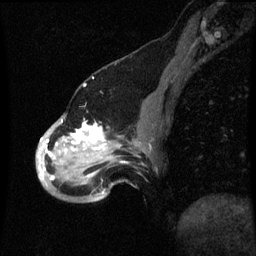
Breast MRI (dynamic contrast-enhanced), one sagittal slice; position 20 of 60 along the scan axis; dynamic contrast-enhanced series, image 2 of 3 at this slice position (ordered by acquisition); 1.5 T; TE 4.2 ms, TR 8.9 ms; 2 mm slice thickness; 256 × 256 image matrix. Female patient, age 49 years. From the clinical record (not read from this slice): setting: breast cancer imaged before/during neoadjuvant chemotherapy; receptor status: HR-positive, HER2-negative.
Outlined on this slice (semi-automatically segmented with operator editing):
- analysis volume of interest (the breast-tissue region the enhancement analysis was run in; not a lesion): bounding box <36,114,147,199> (left, top, right, bottom; pixels)
- tumour enhancement mask (voxels above the 70 % enhancement threshold inside the analysis volume of interest): <36,122,107,181>